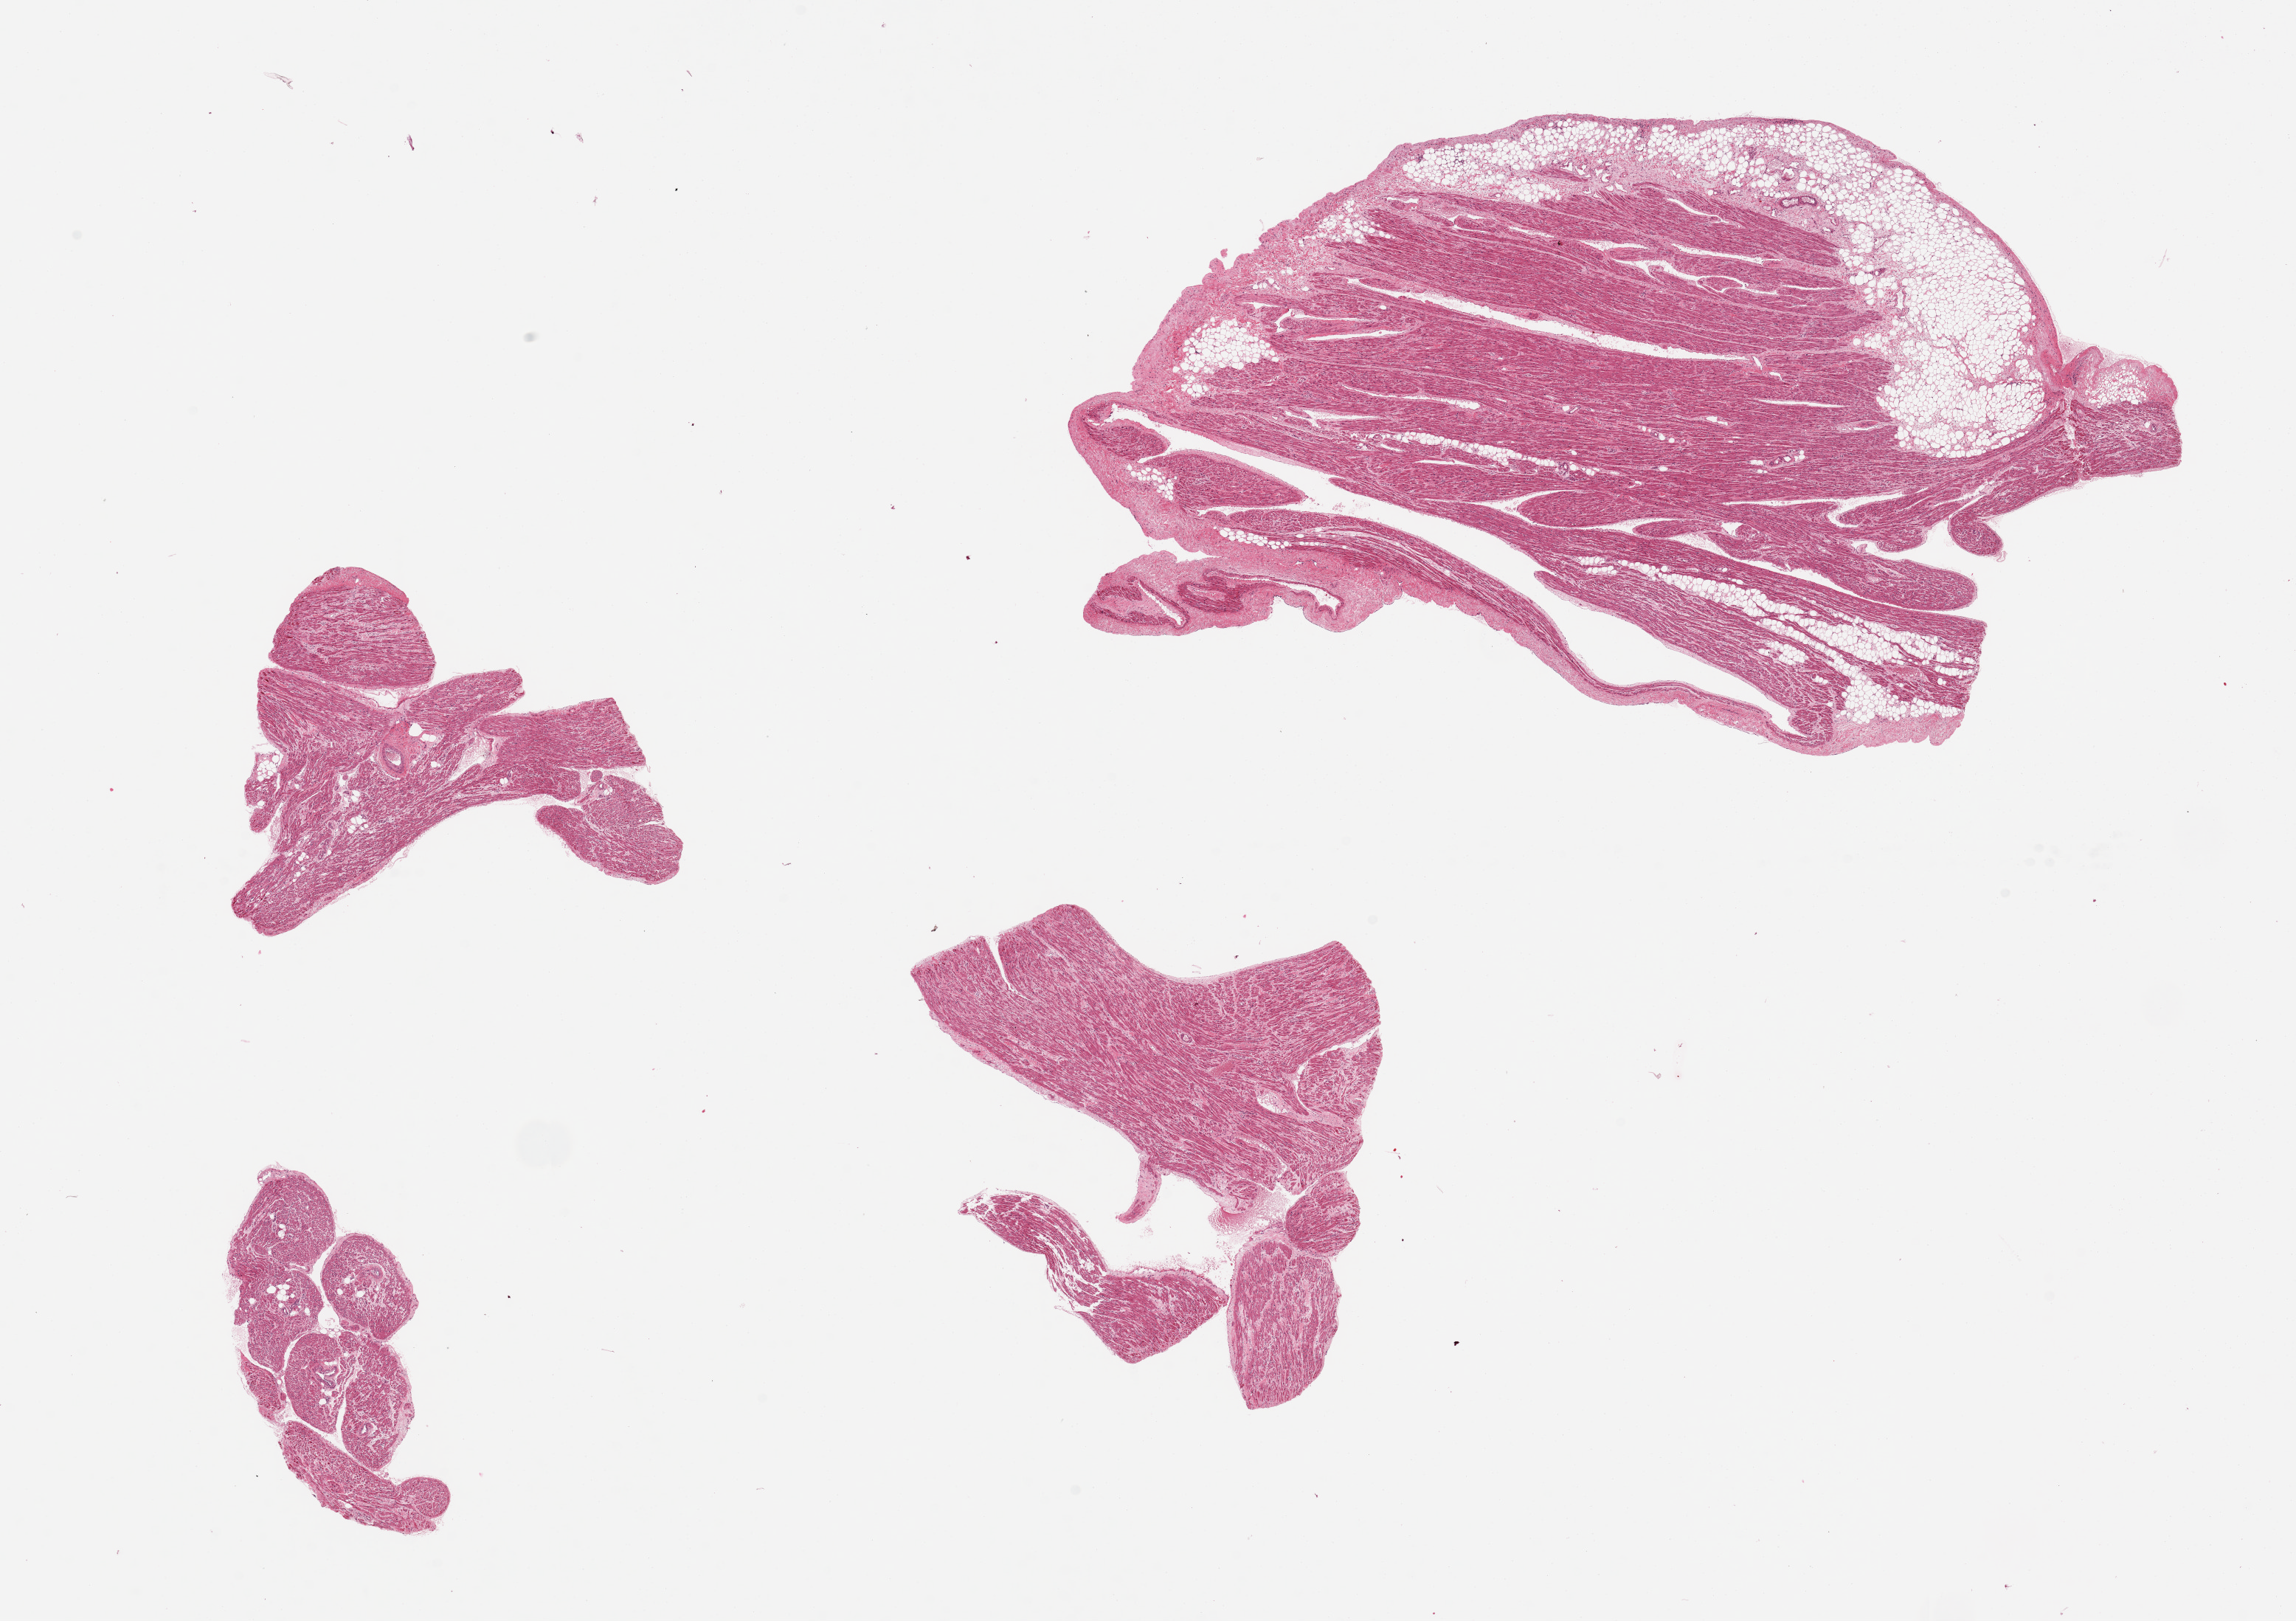
H&E whole-slide image, whole scanned area (about 24.6 x 17.4 mm) shown as a low-resolution overview. PAXgene-fixed paraffin-embedded (PFPE) section. Sampled site (target tissue): auricular appendage. Donor tissue sample. Female donor.
Pathologist's review note for this sample: 4 pieces; appears to represent atrial appendage specimen, not left ventricle. Increased interstitial fibrosis, largest piece is 20% fat.